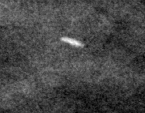
Crop from a digitized film mammogram around one marked abnormality, left breast, CC view.
Calcifications, distribution regional; BI-RADS assessment category 2; benign; no additional work-up was recommended (benign without callback).